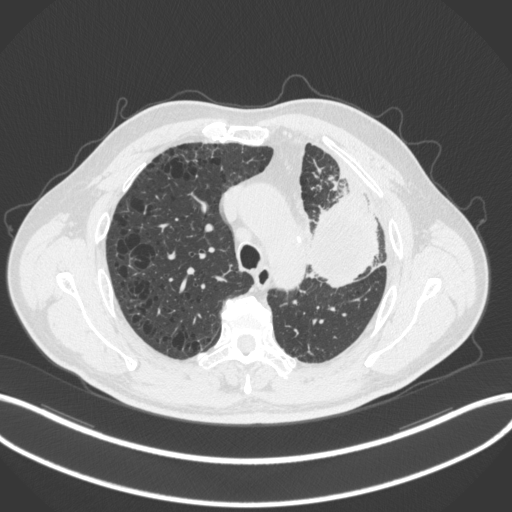
Chest CT, one axial slice; slice 215 of 286 in the series (ordered by position); reconstruction kernel B31f; lung window (W 1500 / L -600 HU); 1 mm slice thickness; 512 × 512 image matrix. Male patient, age 68 years. Case-level facts recorded for this patient, not image findings: clinical TNM (as recorded): T3 N3 M1.
Structures marked on this image (rectangle marked by the reading radiologist):
- lung tumour (recorded histology: adenocarcinoma): bounding box <305,180,386,292> (left, top, right, bottom; pixels)